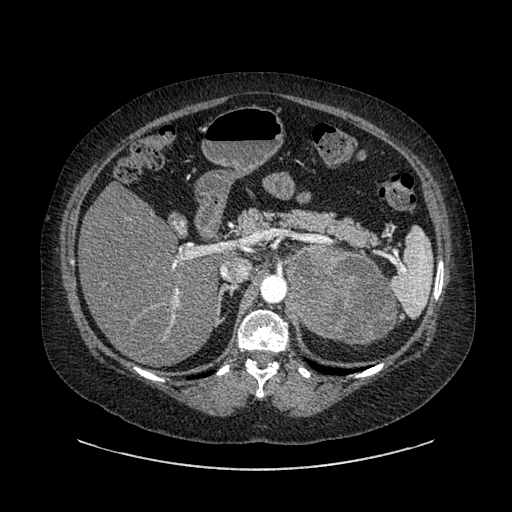
Contrast-enhanced abdominal CT, one axial slice. Position 580 of 769 along the scan axis. Reconstruction kernel SOFT. Intravenous contrast given. Soft-tissue window (W 400 / L 40 HU). 512 × 512 image matrix, field of view 460 × 460 mm. Female patient, age 61 years. From the clinical record (not read from this slice): diagnosis: adrenocortical carcinoma; tumour side: left adrenal.
Outlined on this slice (semi-automatically segmented with operator editing):
- mass: bounding box <288,247,393,344> (left, top, right, bottom; pixels)